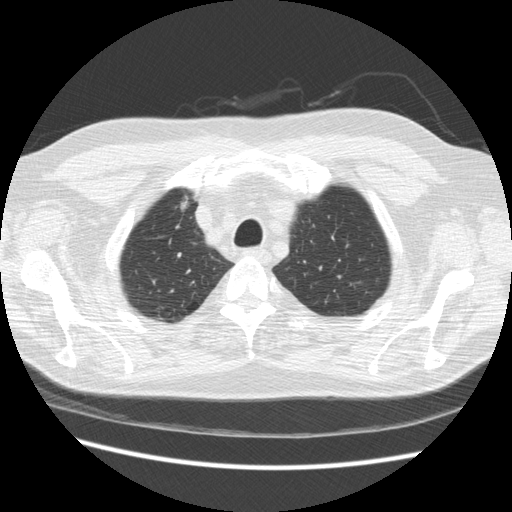
Low-dose screening chest CT, axial slice; third screening round (two years after baseline); lung window (W 1500 / L -600 HU); 2.5 mm slice thickness; standard (soft-tissue) reconstruction kernel (STANDARD); slice 41 of 234 in the series; 512 × 512 image matrix. Male, age 66 years at enrolment. Former smoker at enrolment.
• Expert-annotated lung lesion, bounding box [x1, y1, x2, y2] px = [167, 188, 206, 221].
• No non-calcified nodule or mass ≥4 mm was recorded by the screening reader at this exam.
• Official screen result: positive, other.
• Participant outcome: lung cancer diagnosed 229 days after this screen — bronchiolo-alveolar adenocarcinoma, NOS, right upper lobe, moderately differentiated (G2), stage IA (AJCC 6th edition), 12 mm at pathology.